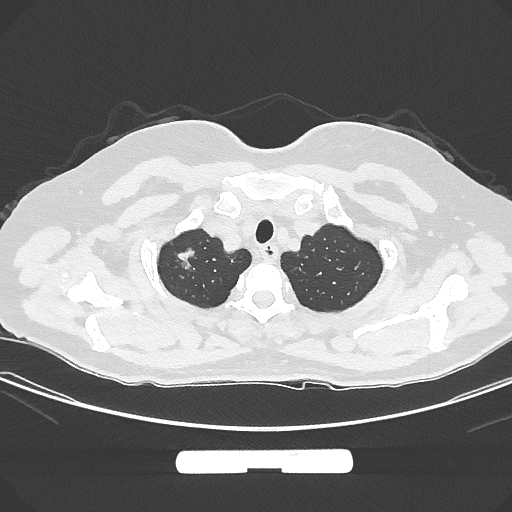
Chest CT, one axial slice; slice 263 of 294 in the series (ordered by position); reconstruction kernel IMR1,SharpPlus; 120 kVp; lung window (W 1500 / L -600 HU); 1 mm slice thickness; 512 × 512 image matrix. Patient: female, 58 years. From the clinical record (not read from this slice): clinical TNM (as recorded): T1b N0 M0.
Outlined on this slice (rectangle marked by the reading radiologist):
- lung tumour (recorded histology: adenocarcinoma): bounding box <171,243,205,277> (left, top, right, bottom; pixels)